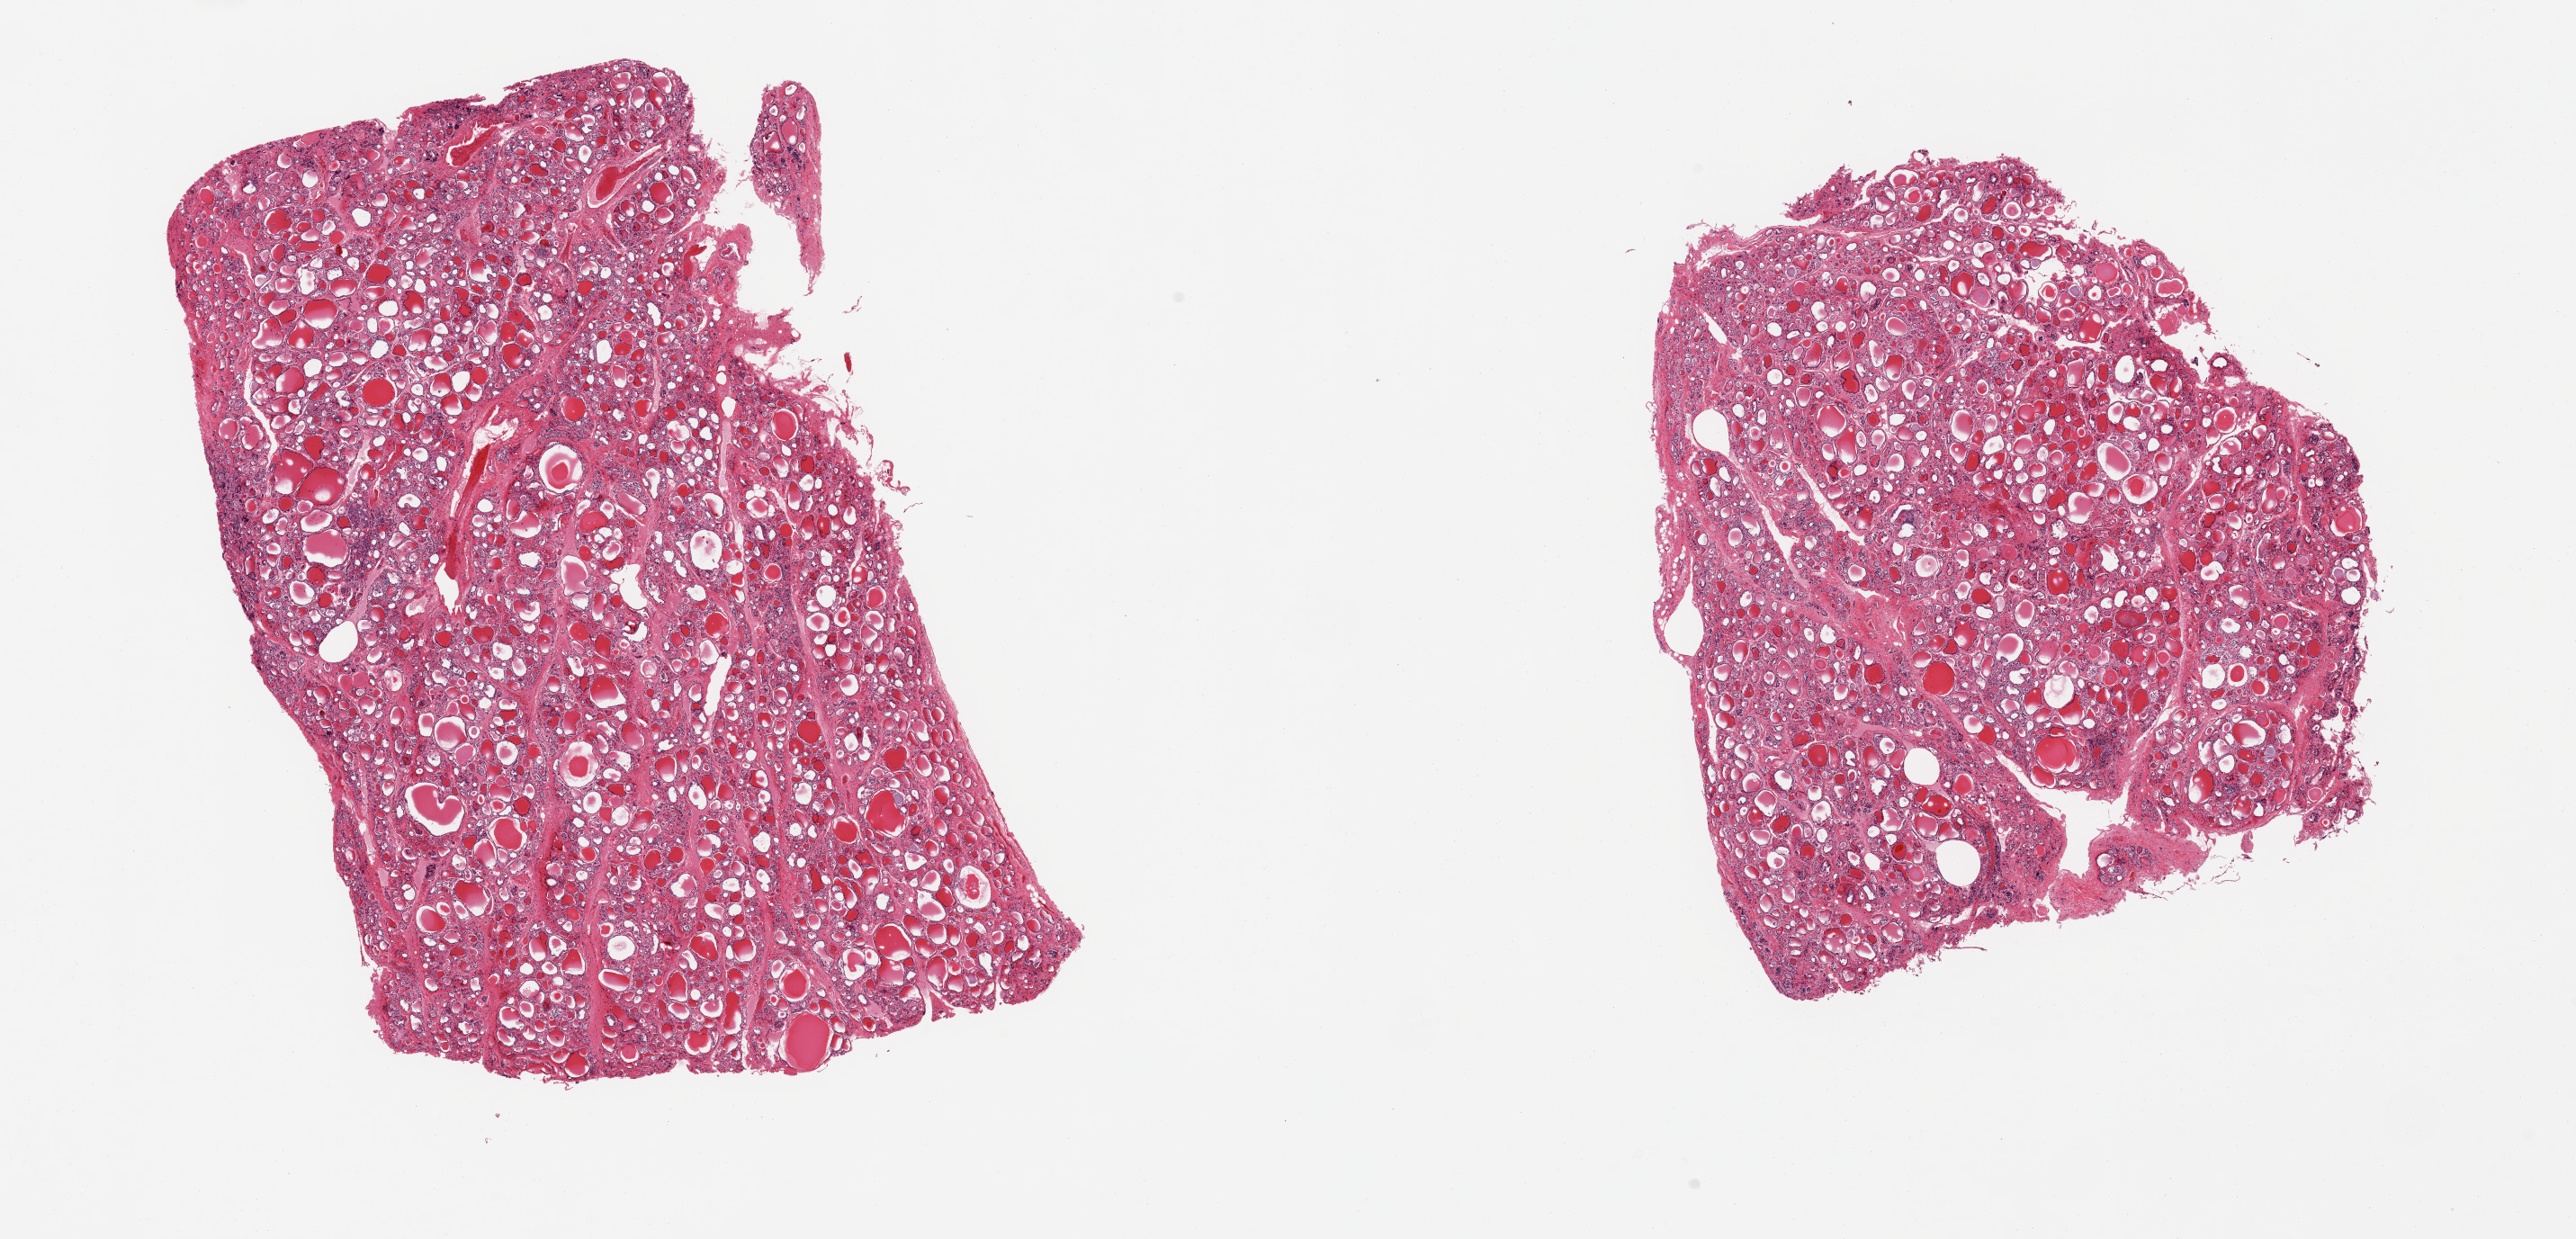
Whole-slide image, H&E stain — whole scanned area (about 22.6 x 10.9 mm) shown as a low-resolution overview; PAXgene-fixed, paraffin-embedded tissue; target tissue: thyroid; tissue donor sample.
Reviewer comment on this tissue sample: 2 pieces; preserved follicular architecture with some evidence of hyperplasia.